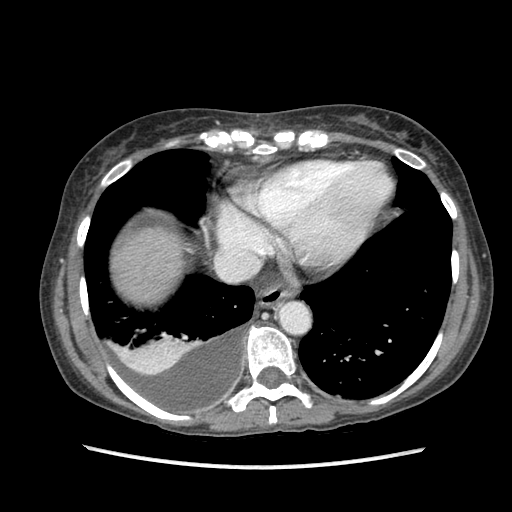
Contrast-enhanced abdominal CT (liver protocol), one axial slice; slice 81 of 87 in the series (ordered by position); 120 kVp; soft-tissue window (W 400 / L 40 HU); 2.5 mm slice thickness; 512 × 512 image matrix, field of view 340 × 340 mm. From the clinical record (not read from this slice): diagnosis: hepatocellular carcinoma (patient treated with transarterial chemoembolisation; whether this scan precedes or follows treatment is not stated here); TNM stage (as recorded): Stage-IIIB; Child-Pugh class: A; tumour differentiation: no biopsy.
Structures marked on this image (semi-automatically segmented with operator editing):
- liver parenchyma outside the tumour (the mass and vessels are separate outlines, so this box may not span the whole liver): bounding box <112,228,182,302> (left, top, right, bottom; pixels)